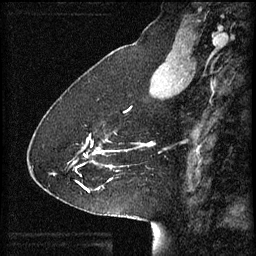
Breast MRI (dynamic contrast-enhanced), one sagittal slice. Slice 21 of 60 in the series (ordered by position). 3 images stored at this slice position (order not interpretable as contrast timing). 1.5 T. TE 4.2 ms, TR 8.2 ms. 256 × 256 image matrix, field of view 200 × 200 mm. Patient: female, 41 years.
Annotated regions visible in this slice (semi-automatically segmented with operator editing):
- analysis volume of interest (the breast-tissue region the enhancement analysis was run in; not a lesion): bounding box (x1, y1, x2, y2) in pixels: (69, 132, 128, 181)
- tumour enhancement mask (voxels above the 70 % enhancement threshold inside the analysis volume of interest): (69, 134, 120, 181)